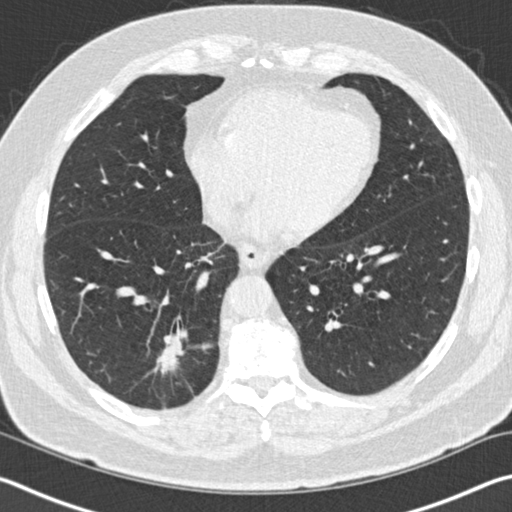
Low-dose screening chest CT, one axial slice. Position 40 of 141 along the scan axis. Reconstruction kernel B30f. 120 kVp. Lung window (W 1500 / L -600 HU). 2 mm slice thickness. 512 × 512 image matrix, field of view 344 × 344 mm.
Annotated regions visible in this slice (manually delineated by an expert):
- lesion 1 (tumor, lower lobe of right lung): bounding box (x1, y1, x2, y2) in pixels: (156, 330, 189, 374)